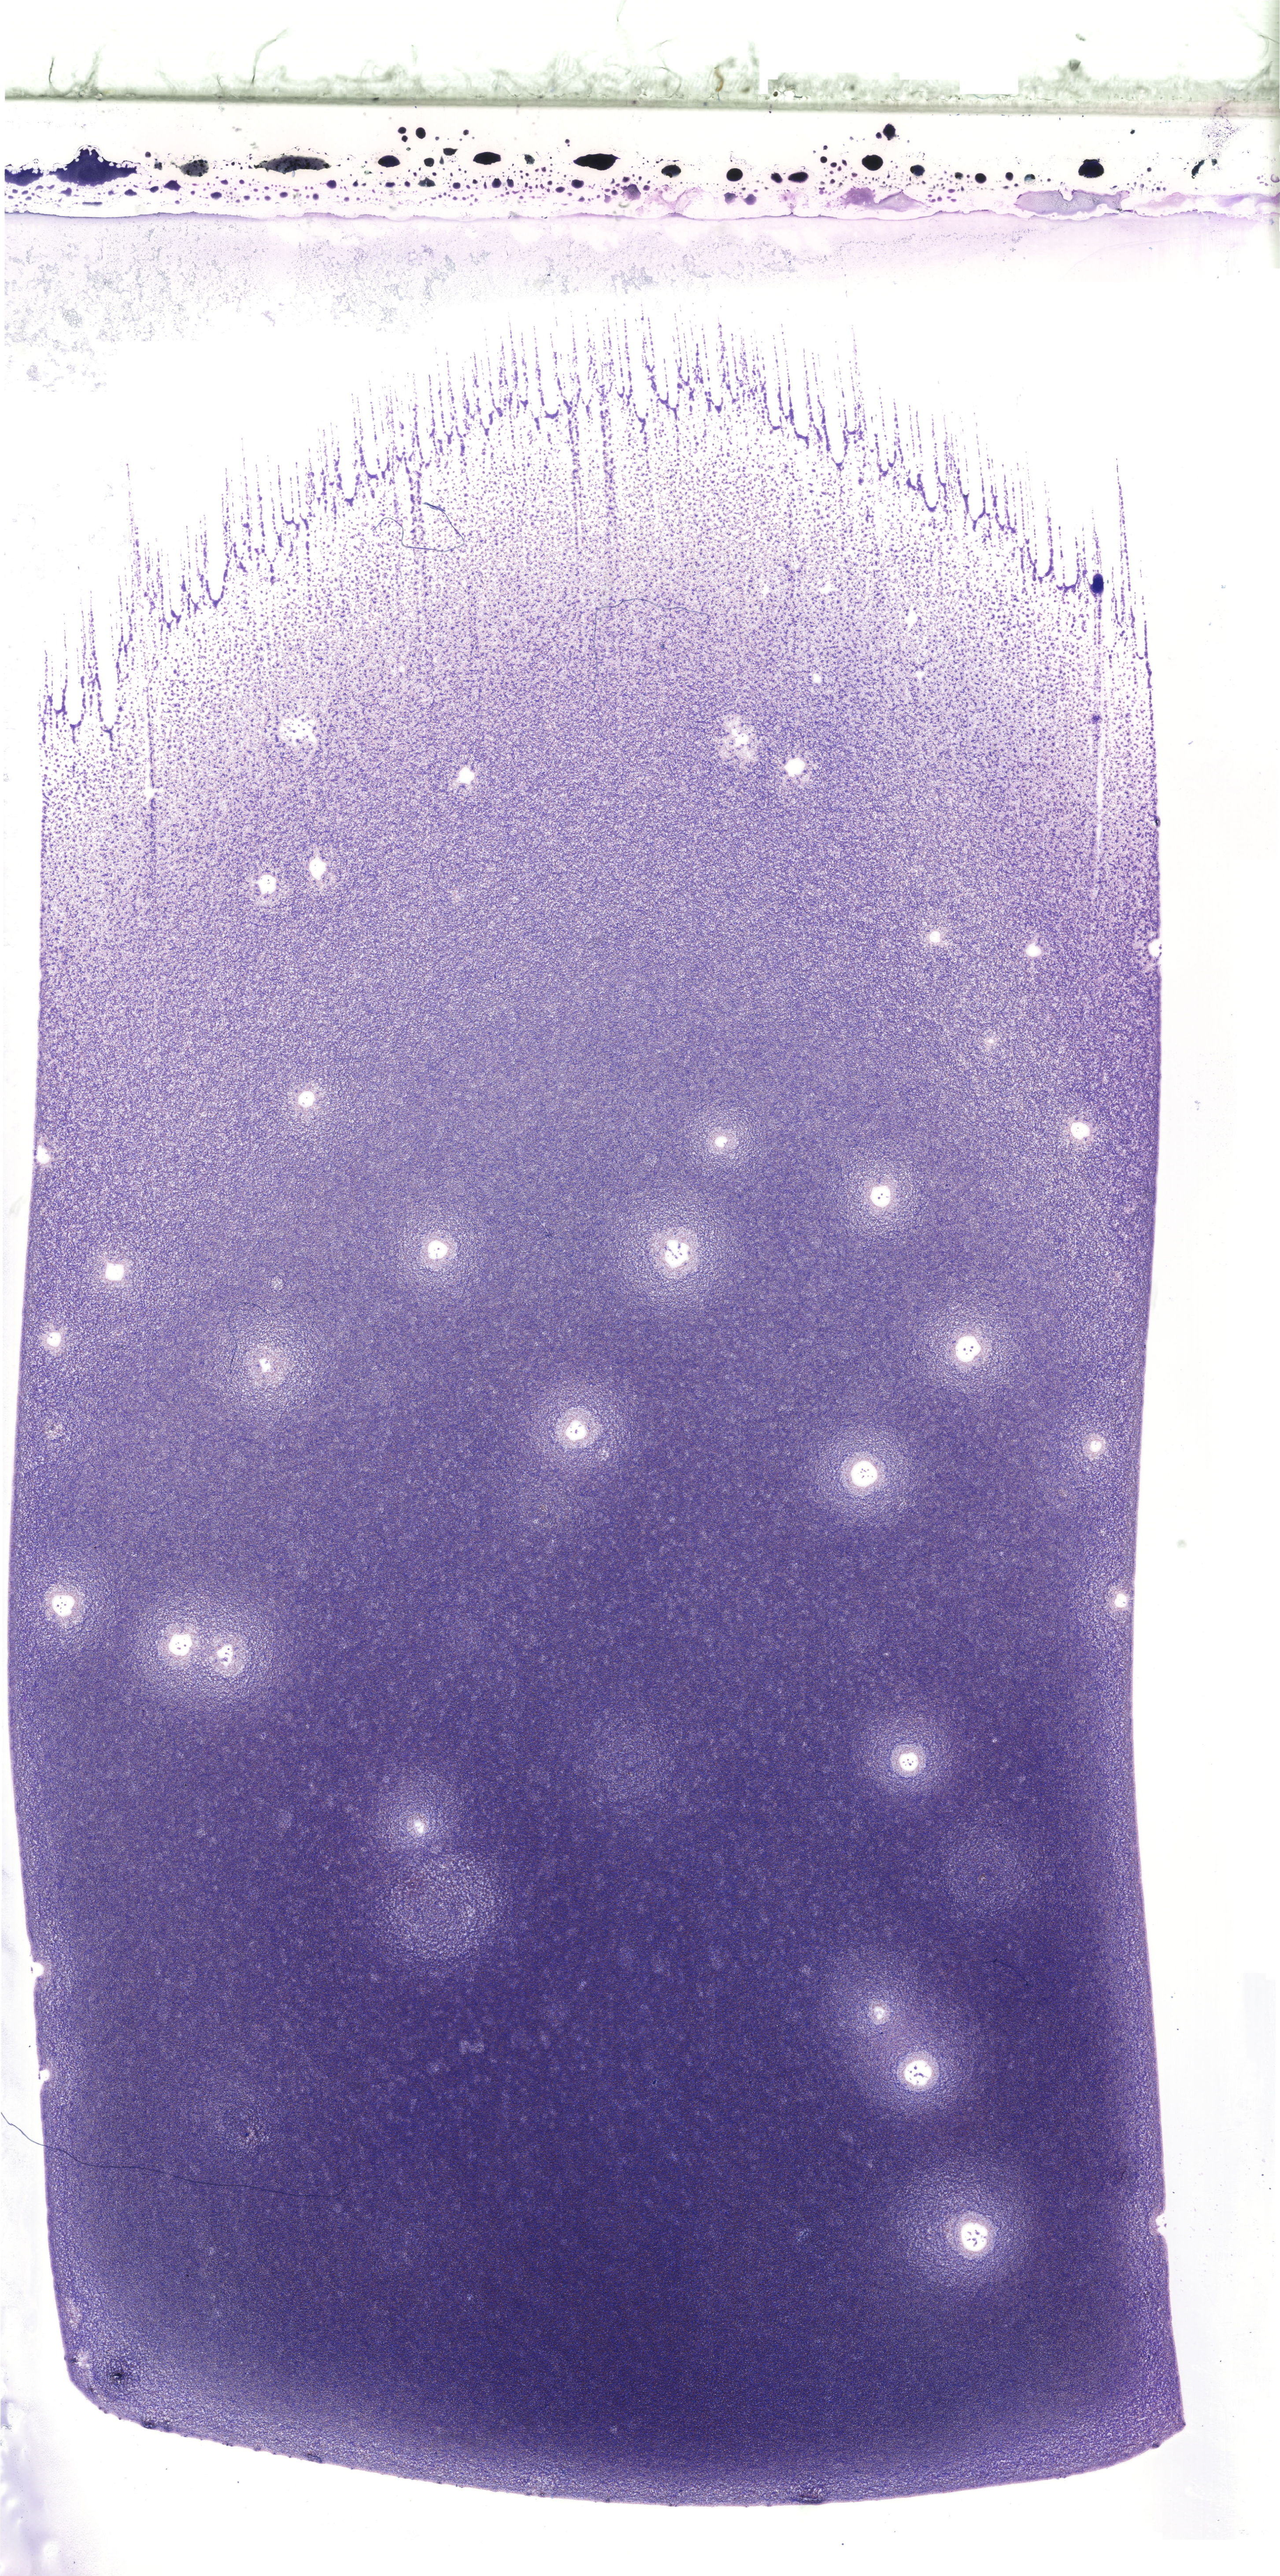
Bone marrow aspirate smear, May-Grünwald–Giemsa stain, whole-slide image, shown as a low-resolution overview of the whole scanned area (about 20.6 x 41.4 mm). Patient sex: male.
- diagnosis: Acute Myeloid Leukemia without Maturation